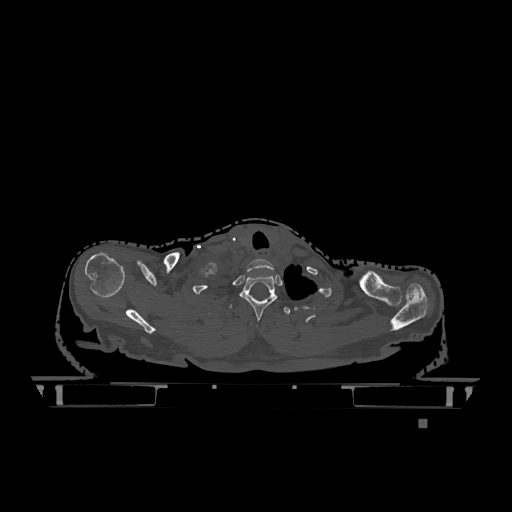
CT including the spine, one axial slice. Slice 995 of 1317 in the series (ordered by position). Bone window (W 1800 / L 400 HU). 0.5 mm slice thickness. 512 × 512 image matrix, field of view 500 × 500 mm. Patient: female, 74 years. Case-level facts recorded for this patient, not image findings: primary cancer: lung; vertebrae with lytic lesions (as recorded): T1, T4, T5, T6, L4, L5.
Structures marked on this image (semi-automatic segmentation, software-assisted and operator-edited):
- T1 vertebra: bounding box [x1, y1, x2, y2] px = [240, 275, 278, 321]
- T2 vertebra: [229, 304, 291, 315]